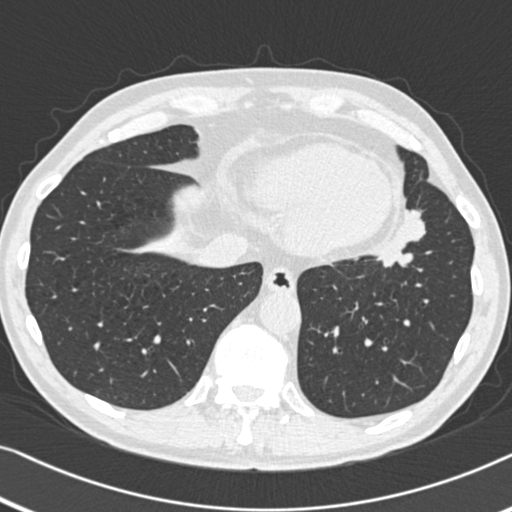
Low-dose screening chest CT, one axial slice; position 127 of 383 along the scan axis; reconstruction kernel B30f; 120 kVp; lung window (W 1500 / L -600 HU); 1 mm slice thickness; 512 × 512 image matrix.
Annotated regions visible in this slice (expert manual segmentation):
- lesion 1 (tumor, upper lobe of left lung): bounding box [x1, y1, x2, y2] px = [377, 210, 425, 267]